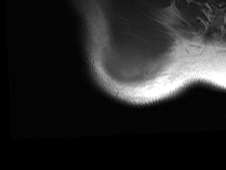
MRI of an extremity soft-tissue mass, one axial slice; slice 59 of 81 in the series (ordered by position); MR volume resampled by the dataset authors to the PET/CT grid (not the native acquisition matrix); 3.27 mm slice thickness; 226 × 170 image matrix, field of view 221 × 166 mm. Male patient. Case-level facts recorded for this patient, not image findings: histological type: pleiomorphic spindle cell undifferentiated; grade: high; site of the primary tumour: right parascapusular.
Outlined on this slice (expert contour drawn on MRI and transferred to this co-registered scan by the dataset authors):
- gross tumour volume including surrounding oedema: bounding box (x1, y1, x2, y2) in pixels: (99, 49, 173, 93)
- gross tumour volume (mass): (103, 49, 152, 89)